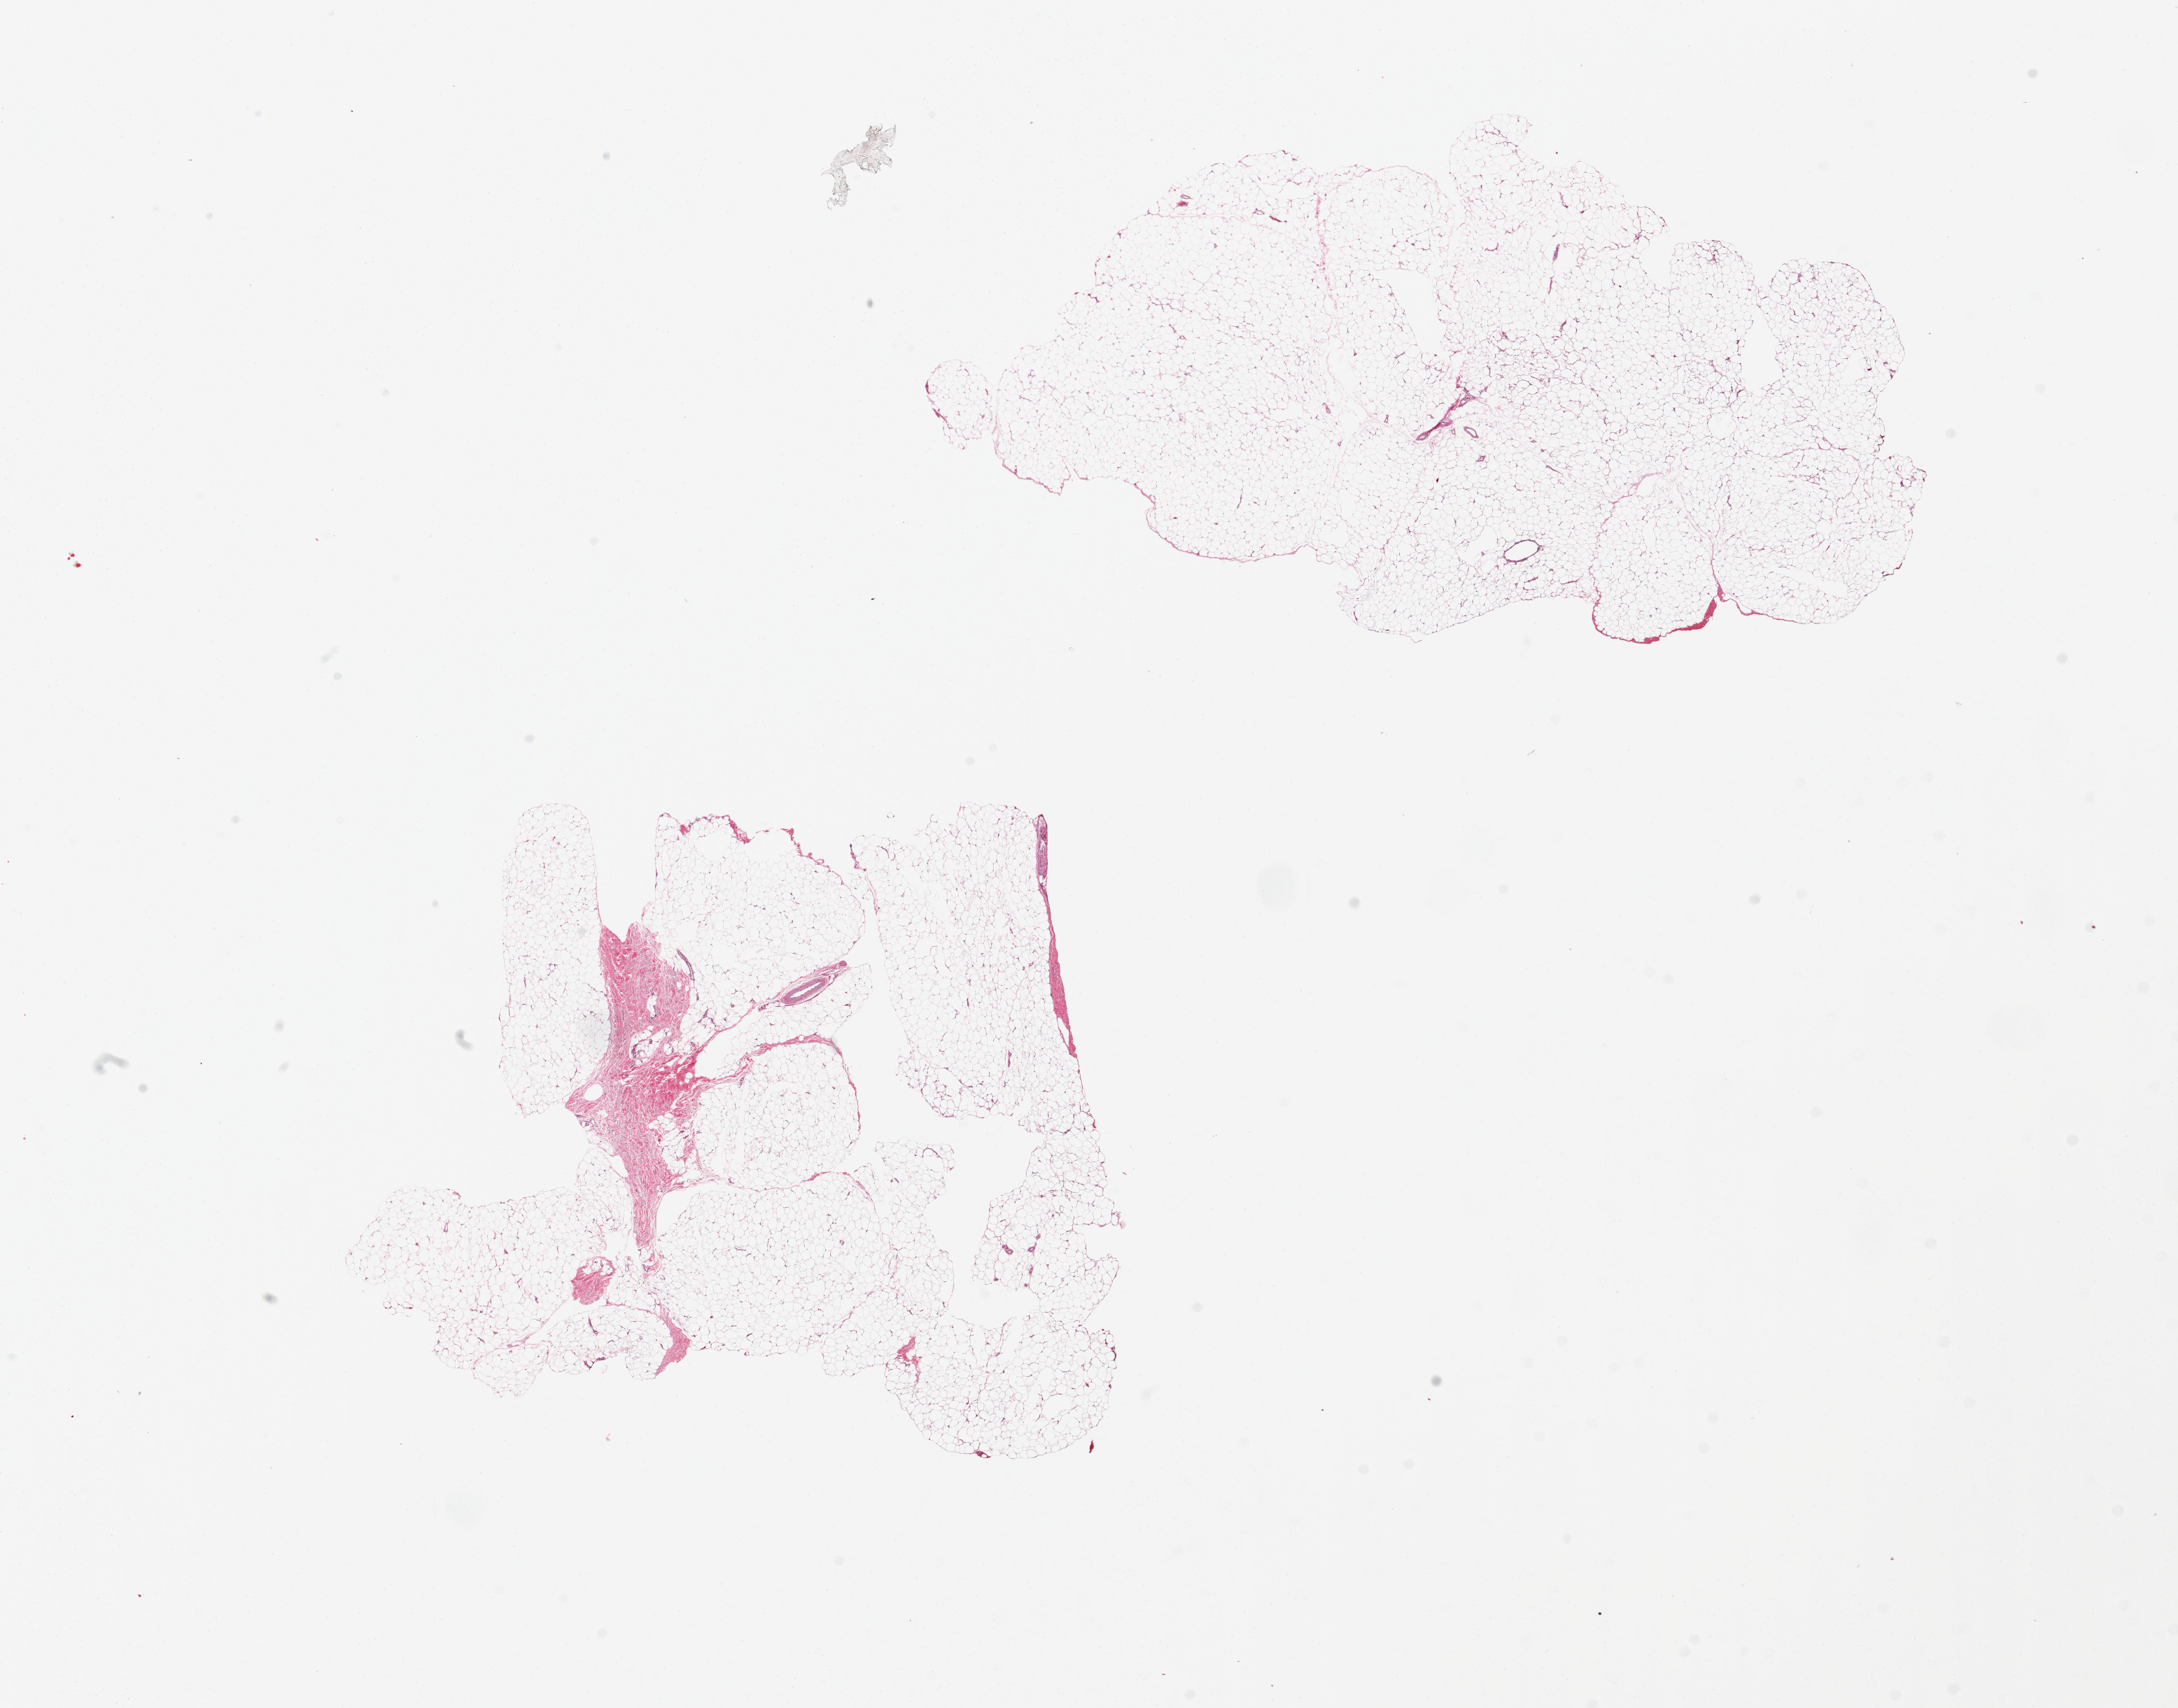
Whole-slide image, haematoxylin and eosin stain — a low-resolution overview of the entire scanned area, about 24.6 x 19.3 mm, PAXgene-fixed paraffin-embedded (PFPE) section, sampled site (target tissue): adipose tissue, tissue donor sample. Donor sex: male.
Pathologist's review note for this sample: 2 pieces, one is ~10% fibrous tissue.